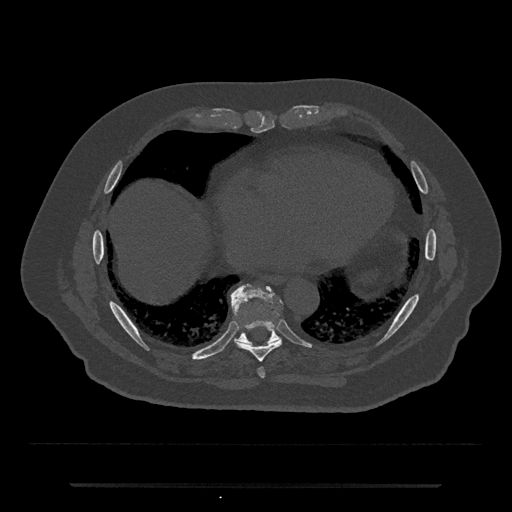
CT including the spine, one axial slice. Slice 790 of 797 in the series (ordered by position). Reconstruction kernel Br40s/3. 120 kVp. Bone window (W 1800 / L 400 HU). 512 × 512 image matrix, field of view 434 × 434 mm. Male patient, age 80 years. Case-level facts recorded for this patient, not image findings: primary cancer: prostate.
Annotated regions visible in this slice (semi-automatic segmentation, software-assisted and operator-edited):
- T8 vertebra: bounding box <236,319,281,362> (left, top, right, bottom; pixels)
- T9 vertebra: <231,284,281,348>